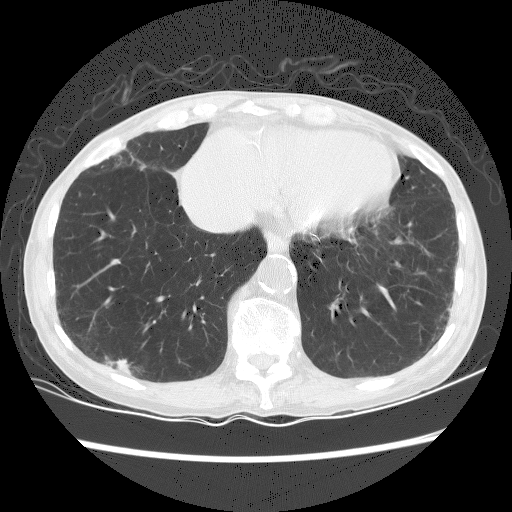
Low-dose screening chest CT, axial slice. Baseline annual screen. Lung window (W 1500 / L -600 HU). 2.5 mm slice thickness. Lung (sharp) reconstruction kernel (BONE). 120 kVp. Slice 101 of 156 in the series. Female participant, aged 70 years at enrolment.
Expert reader's lesion annotation, box from (x=96, y=344) to (x=149, y=385) px. The screening reader recorded 2 non-calcified nodules or masses ≥4 mm on this exam (right lower lobe, left lower lobe); which of them this box marks is not recorded. Lung cancer was diagnosed 125 days after this screen: squamous cell carcinoma, NOS, right lower lobe, well differentiated (G1), stage IA (AJCC 6th edition), 25 mm at pathology.